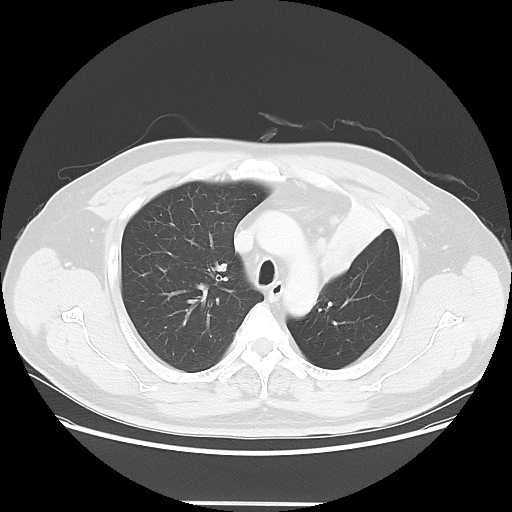
Chest CT, one axial slice. Slice 44 of 62 in the series (ordered by position). Reconstruction kernel LUNG. 120 kVp. Lung window (W 1500 / L -600 HU). 512 × 512 image matrix, field of view 403 × 403 mm. Male patient, age 49 years. From the clinical record (not read from this slice): clinical TNM (as recorded): T3 N3 M1c.
Annotated regions visible in this slice (bounding box drawn by a radiologist):
- lung tumour (recorded histology: squamous cell carcinoma): box from (x=308, y=234) to (x=355, y=286) px